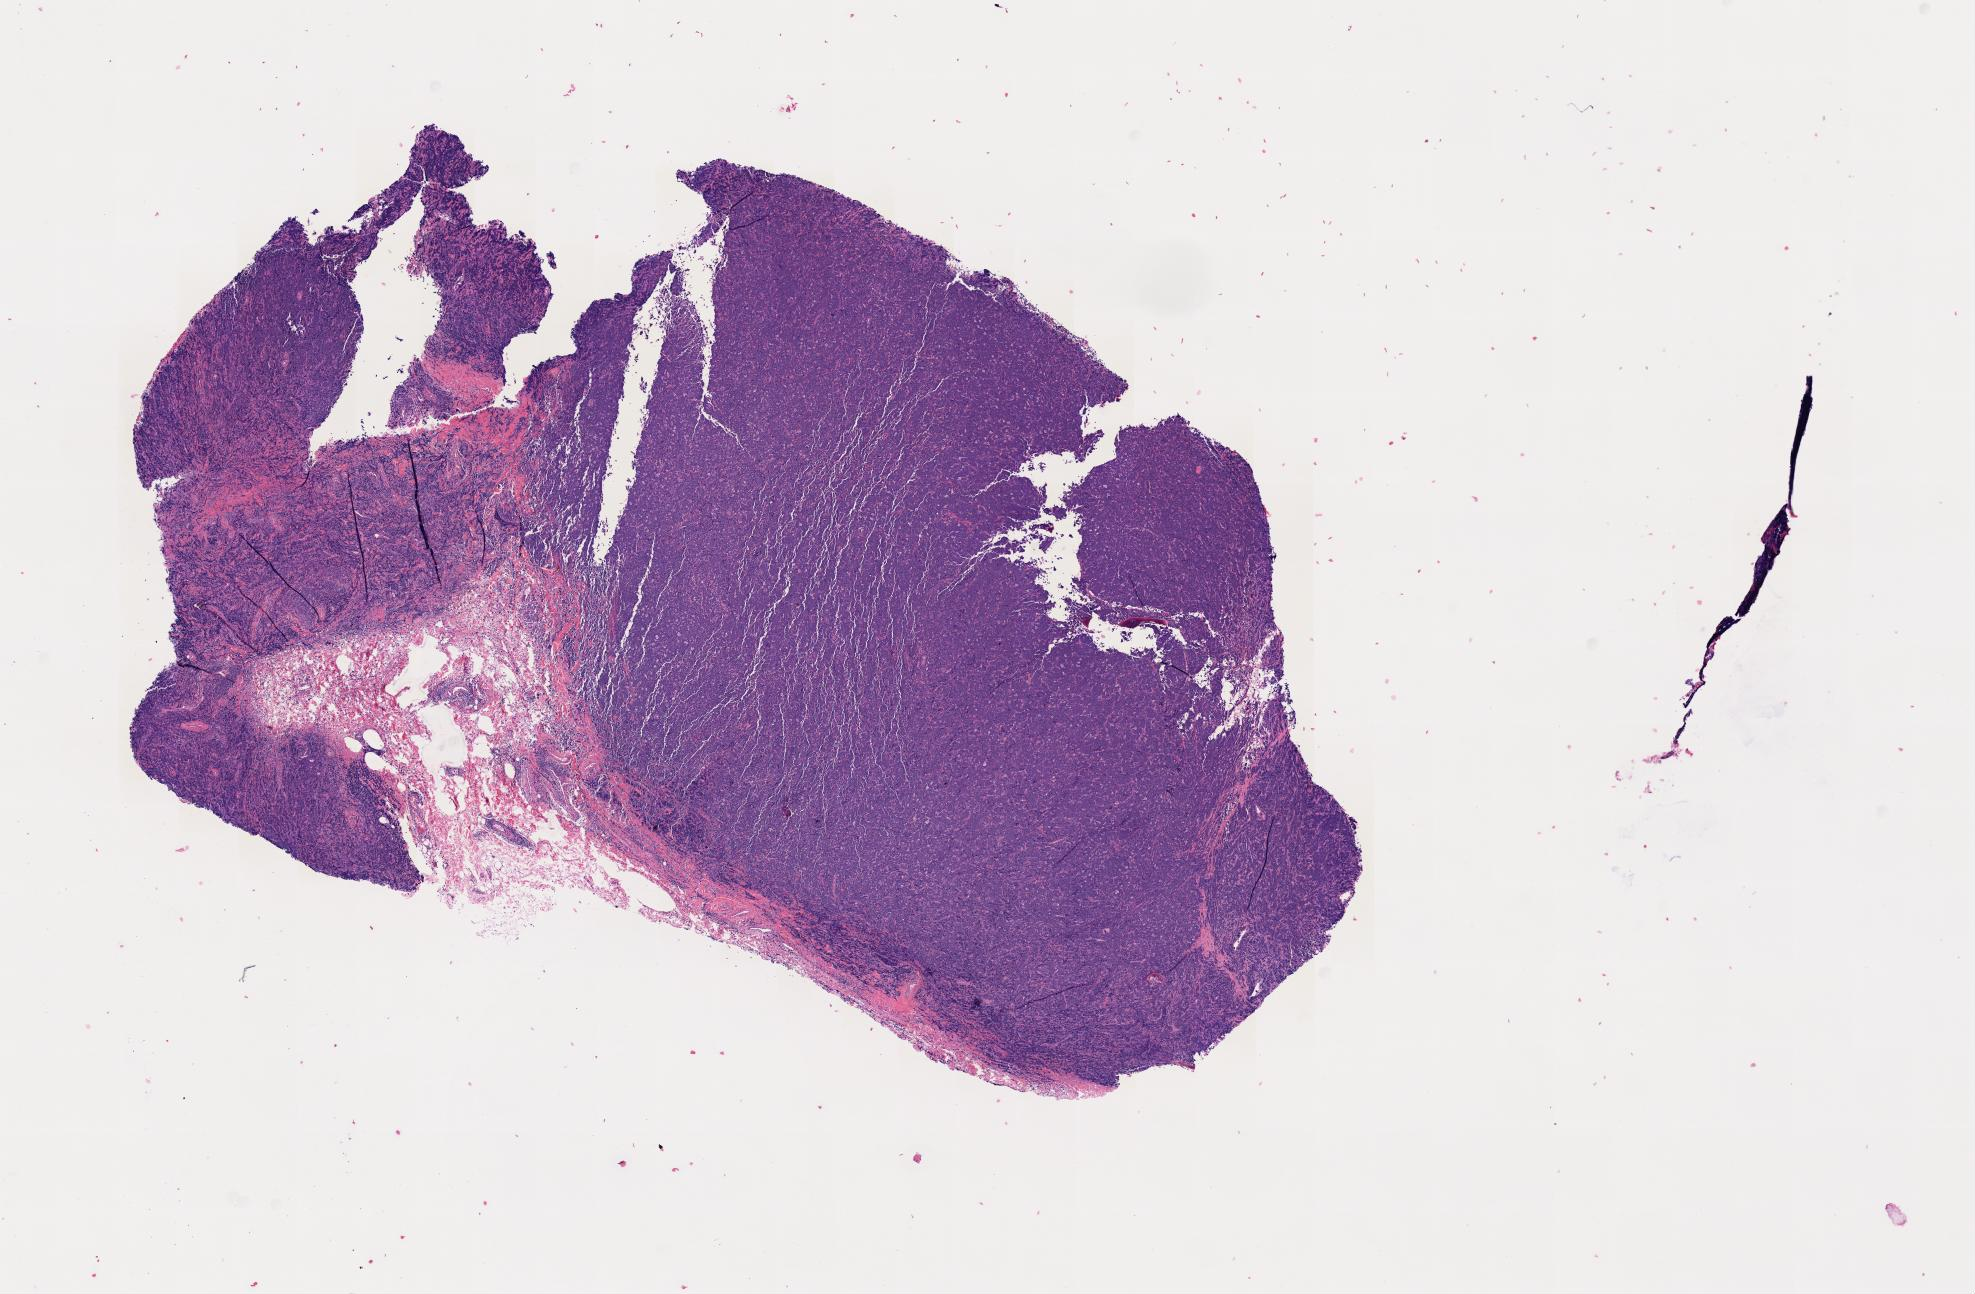
Digitized haematoxylin and eosin-stained section — low-resolution overview of the scanned area, specimen: tumor tissue, site: cranium. Male, age 5 years at initial diagnosis.
Histologic diagnosis: Burkitt lymphoma, NOS.